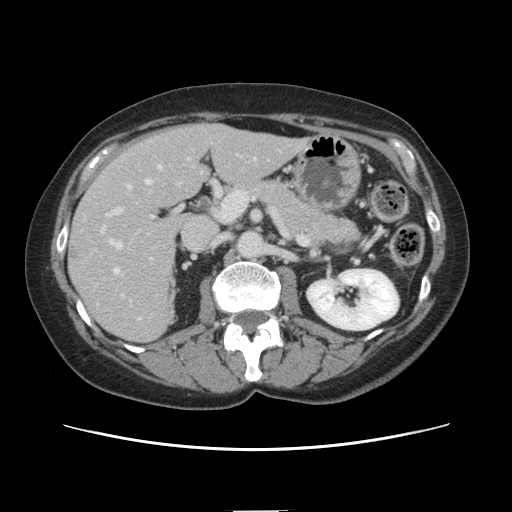
Contrast-enhanced abdominal CT, one axial slice; slice 67 of 141 in the series (ordered by position); 120 kVp; intravenous contrast given; soft-tissue window (W 400 / L 40 HU); 2.5 mm slice thickness; 512 × 512 image matrix, field of view 350 × 350 mm. Female patient, age 63 years. From the clinical record (not read from this slice): diagnosis: colorectal cancer liver metastases, imaged before liver resection; multiple liver metastases: yes; largest metastasis: 3.2 cm; chemotherapy before resection: yes.
Structures marked on this image (outlined manually by an expert reader):
- hepatic veins: bounding box [x1, y1, x2, y2] px = [110, 166, 161, 276]
- liver: [70, 125, 306, 341]
- planned liver remnant (the part of the liver to remain after resection): [176, 125, 307, 190]
- portal vein (with intrahepatic branches): [102, 184, 132, 232]
- liver metastasis: [68, 247, 80, 260]